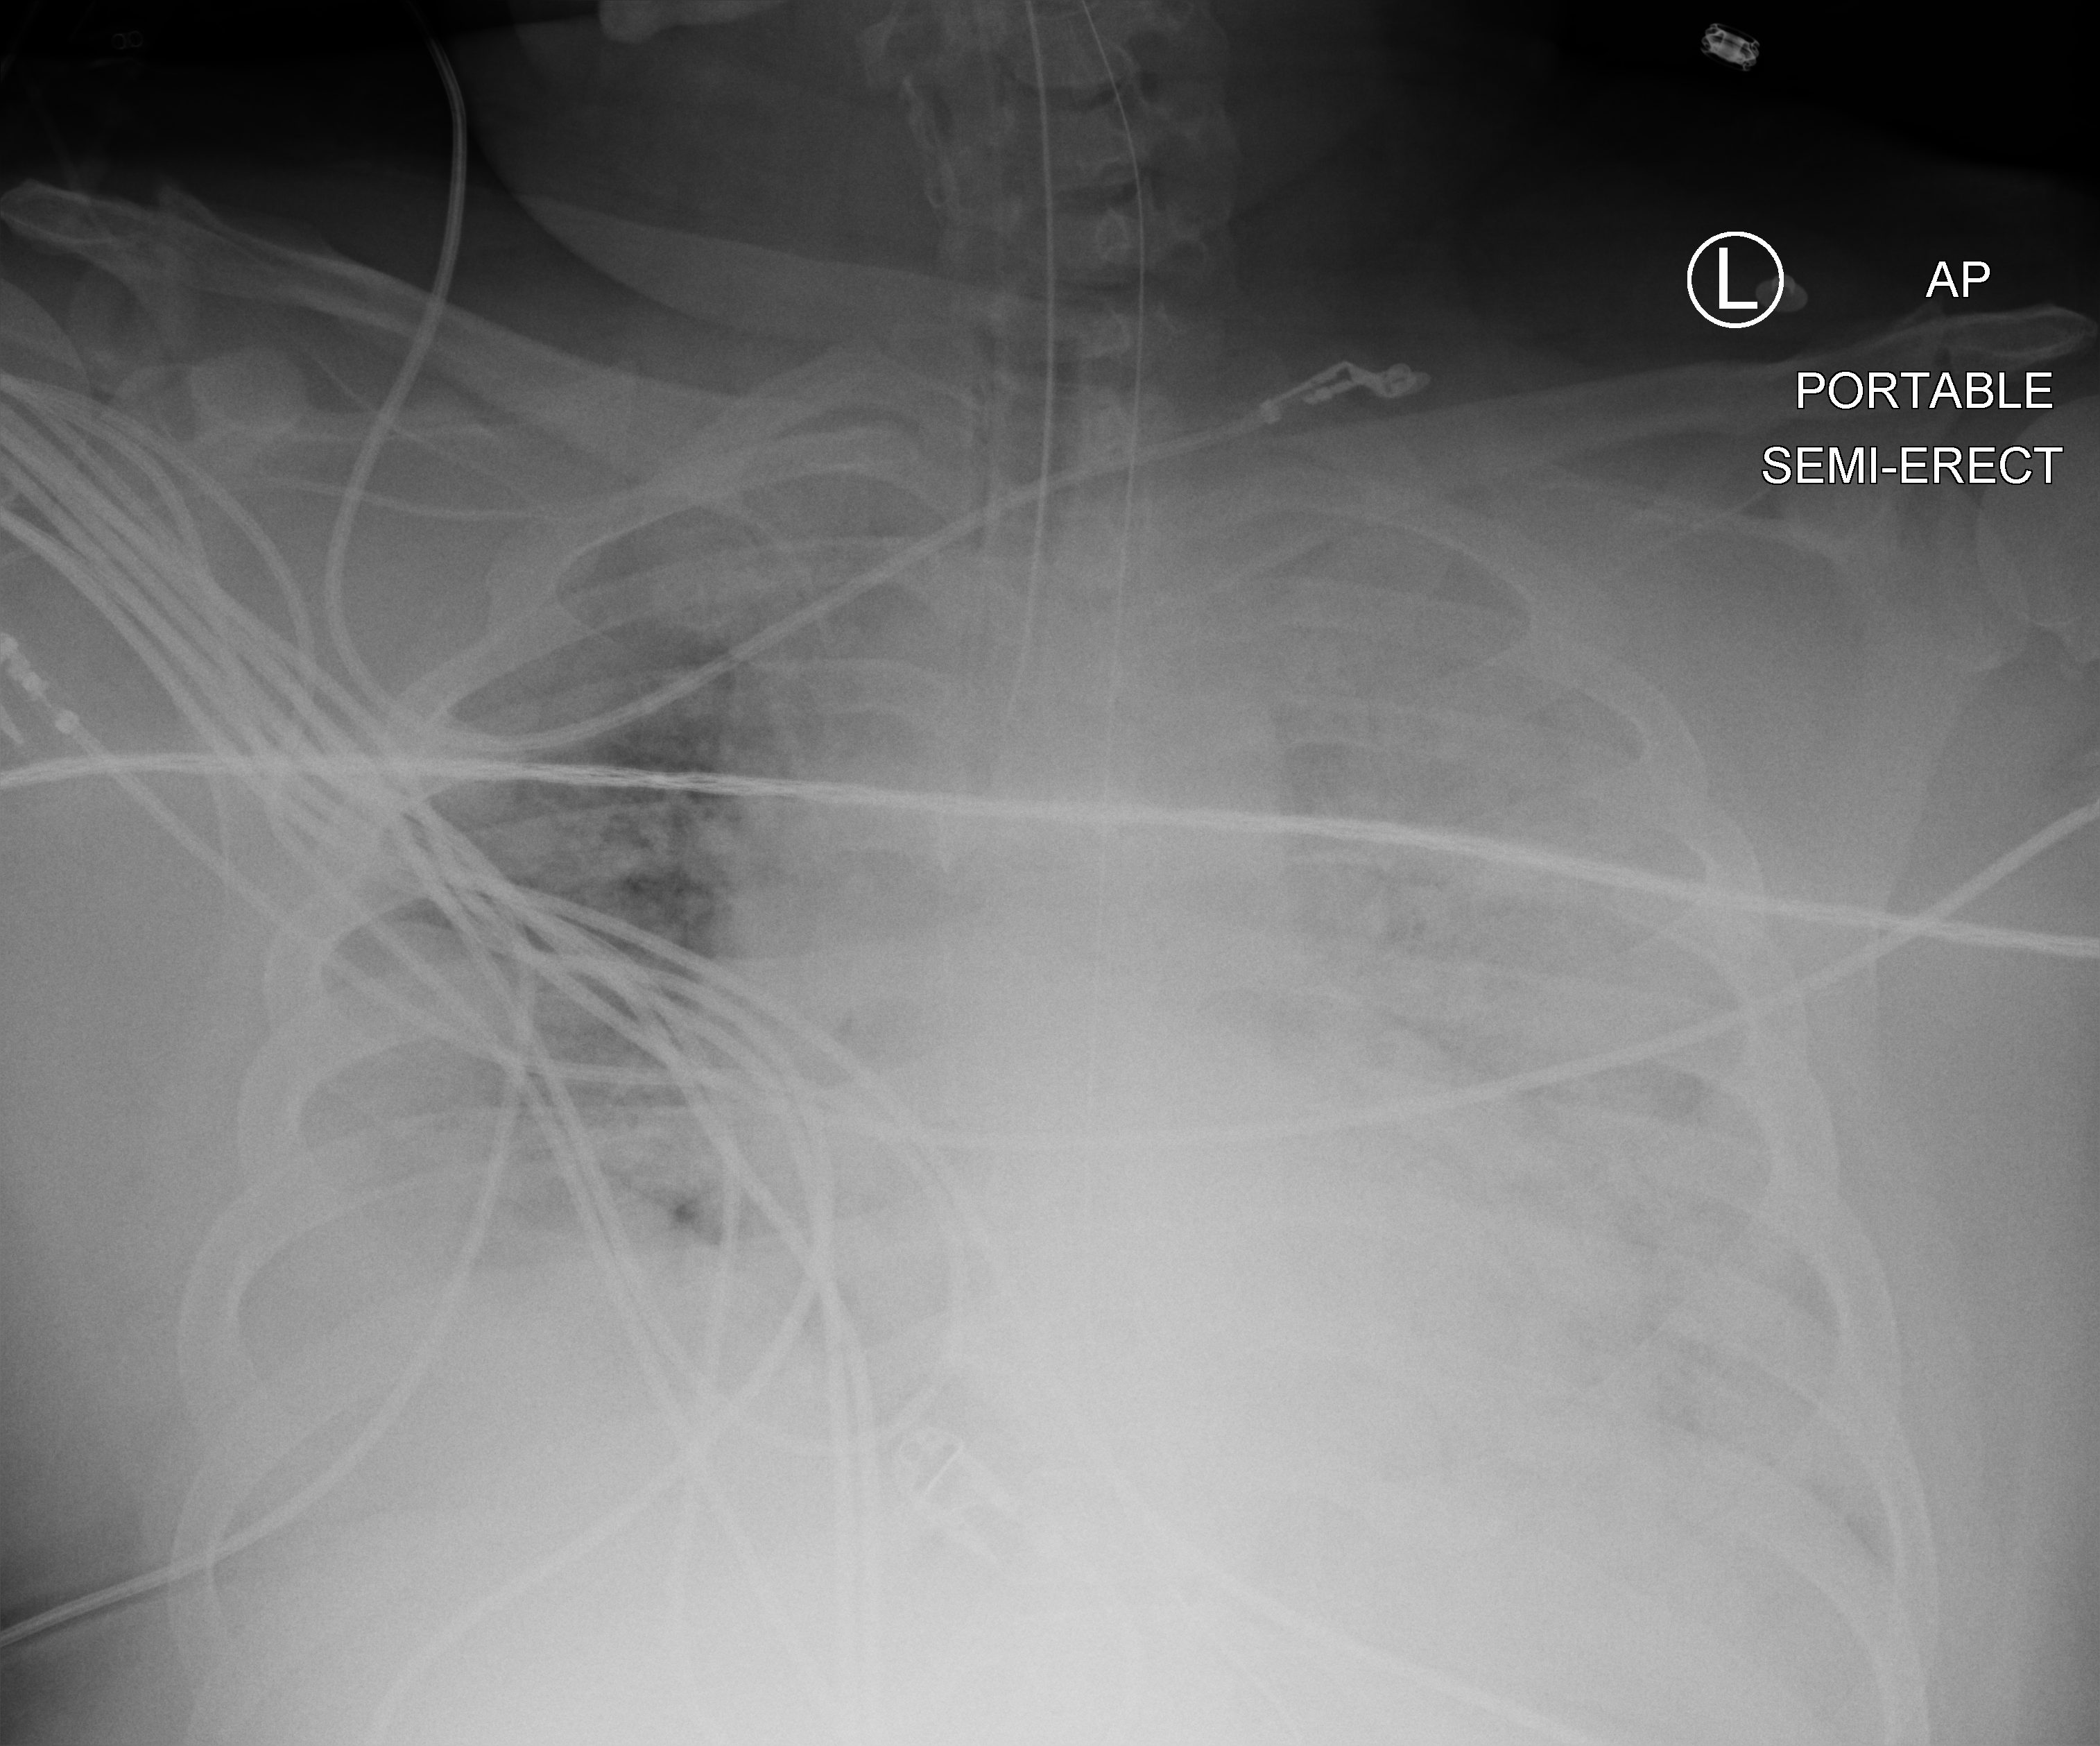
Chest X-ray (portable); anteroposterior (AP) projection. Patient hospitalised with COVID-19, aged 18–59 years.
From the hospital-stay record, not from the radiograph (when in the stay this image was taken is not recorded):
- length of hospital stay: 10 days
- admitted to intensive care during this hospital stay: yes
- mechanically ventilated during this hospital stay: yes